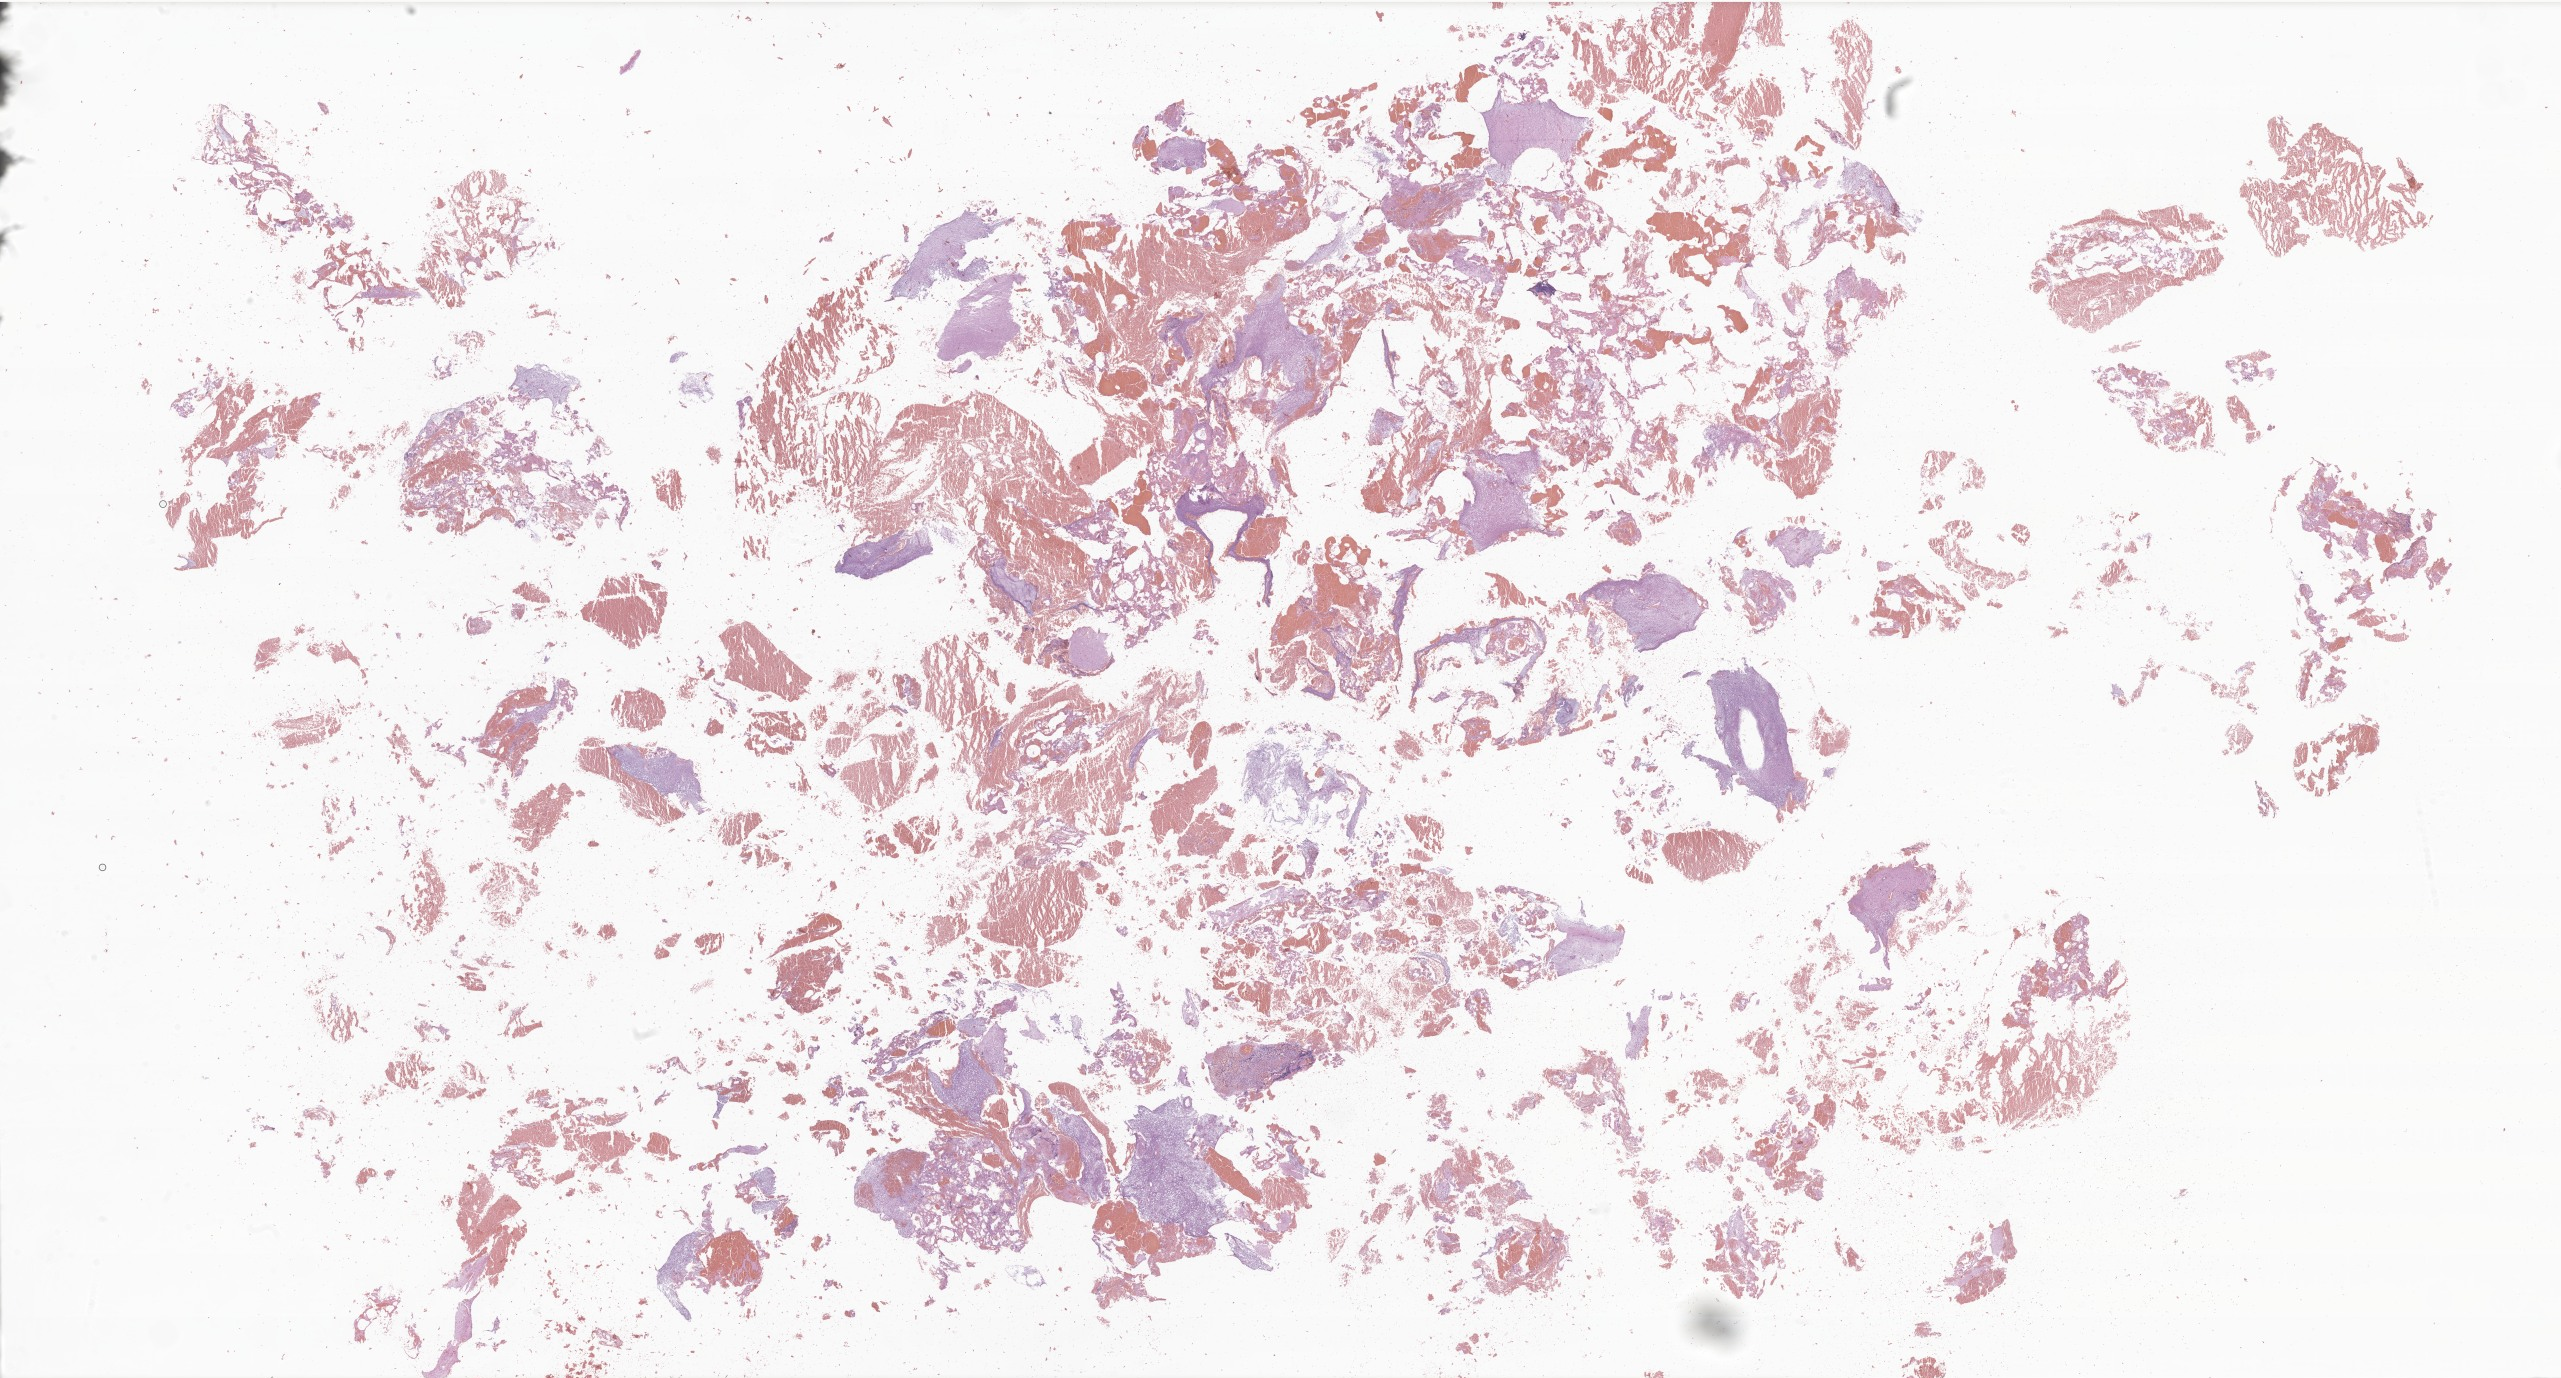
Hematoxylin and eosin (H&E) whole-slide image of tumor tissue from the cerebral ventricle — whole scanned area (about 43.2 x 23.2 mm) shown as a low-resolution overview; FFPE section. Patient female; age 105 months (8 years 9 months).
Diagnosis (ICD-O-3 morphology term): Pilocytic astrocytoma.